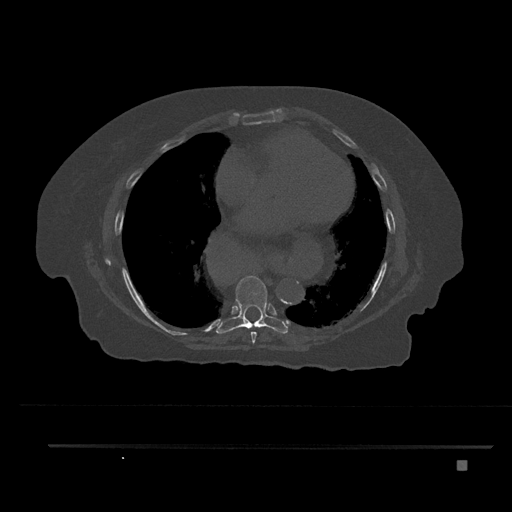
CT including the spine, one axial slice; position 452 of 797 along the scan axis; reconstruction kernel Br40s/3; 120 kVp; bone window (W 1800 / L 400 HU); 0.5 mm slice thickness; 512 × 512 image matrix, field of view 437 × 437 mm. Female patient, age 76 years. From the clinical record (not read from this slice): primary cancer: lung; vertebrae with lytic lesions (as recorded): T11, L3.
Structures marked on this image (semi-automatically segmented with operator editing):
- T7 vertebra: box from (x=250, y=331) to (x=257, y=344) px
- T8 vertebra: (x=216, y=275)–(x=288, y=334)